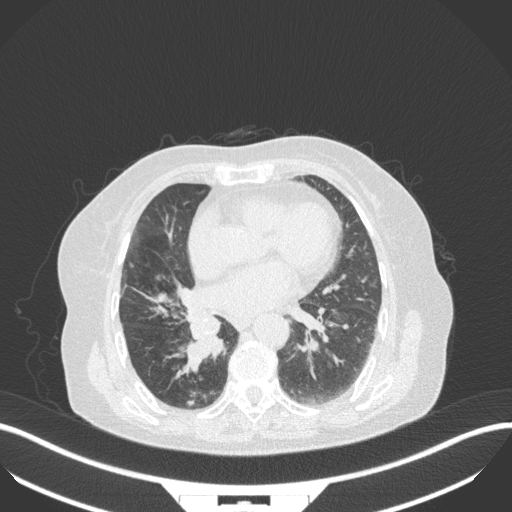
Chest CT, one axial slice. Position 138 of 329 along the scan axis. Reconstruction kernel B31f. 120 kVp. Lung window (W 1500 / L -600 HU). 1 mm slice thickness. 512 × 512 image matrix. Female patient, age 75 years. Case-level facts recorded for this patient, not image findings: clinical TNM (as recorded): T1b N0 M1a.
Structures marked on this image (rectangle marked by the reading radiologist):
- lung tumour (recorded histology: squamous cell carcinoma): bounding box <179,314,223,375> (left, top, right, bottom; pixels)